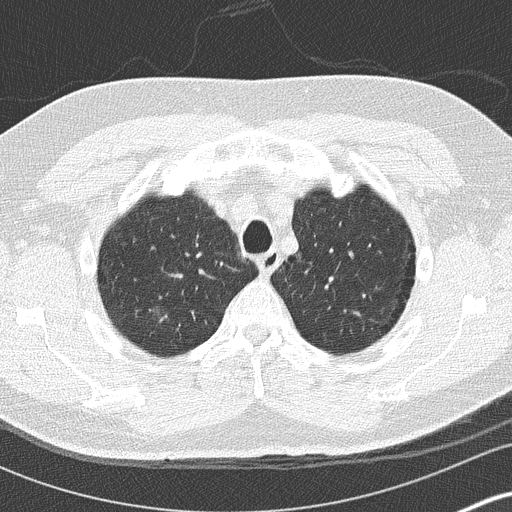
Chest CT (low-dose screening protocol), one axial image, first (baseline) screen, lung window (W 1500 / L -600 HU), lung (sharp) reconstruction kernel (B50f), 512 × 512 image matrix, field of view 310 × 310 mm. Male participant, aged 59 years at enrolment. Current smoker at enrolment.
Expert-annotated lung lesion, bounding box (x1, y1, x2, y2) in pixels: (141, 294, 191, 342). The exam's reader record, not a measurement of the box and not confirmed to be the same lesion: non-calcified nodule or mass ≥4 mm, right upper lobe, 16 × 16 mm, ground glass attenuation. Participant outcome: lung cancer diagnosed 456 days after this screen (after the second annual screen) — bronchiolo-alveolar adenocarcinoma, NOS, right lower lobe, stage IA (AJCC 6th edition), 15 mm at pathology.